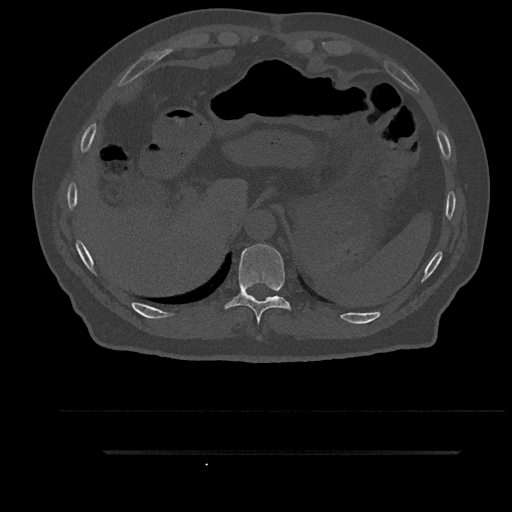
CT including the spine, one axial slice. Position 361 of 797 along the scan axis. Reconstruction kernel Br40s/3. 120 kVp. Bone window (W 1800 / L 400 HU). 0.5 mm slice thickness. 512 × 512 image matrix, field of view 432 × 432 mm. Male patient, age 63 years. Case-level facts recorded for this patient, not image findings: primary cancer: renal.
Outlined on this slice (semi-automatically segmented with operator editing):
- T10 vertebra: bounding box (x1, y1, x2, y2) in pixels: (224, 244, 292, 324)